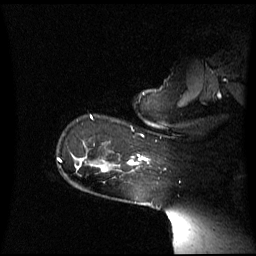
Breast MRI (dynamic contrast-enhanced), one sagittal slice; slice 50 of 60 in the series (ordered by position); dynamic contrast-enhanced series, image 2 of 3 at this slice position (ordered by acquisition); 1.5 T; TE 4.2 ms, TR 8.4 ms; 2.6 mm slice thickness; 256 × 256 image matrix. Patient: female, 39 years. Case-level facts recorded for this patient, not image findings: setting: breast cancer imaged before/during neoadjuvant chemotherapy; receptor status: triple-negative.
Outlined on this slice (semi-automatically segmented with operator editing):
- analysis volume of interest (the breast-tissue region the enhancement analysis was run in; not a lesion): bounding box (x1, y1, x2, y2) in pixels: (117, 156, 148, 171)
- tumour enhancement mask (voxels above the 70 % enhancement threshold inside the analysis volume of interest): (129, 156, 148, 164)